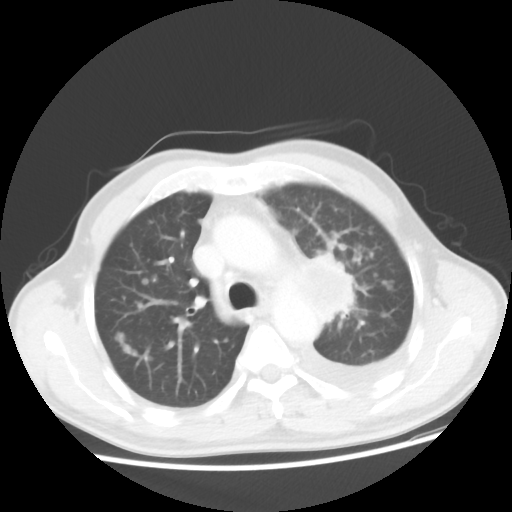
Chest CT, one axial slice; reconstruction kernel STANDARD; lung window (W 1500 / L -600 HU); 512 × 512 image matrix, field of view 362 × 362 mm. Male patient, age 55 years. From the clinical record (not read from this slice): clinical TNM (as recorded): T2 N3 M1a; histopathological grade: G3.
Outlined on this slice (rectangle marked by the reading radiologist):
- lung tumour (recorded histology: squamous cell carcinoma): bounding box [x1, y1, x2, y2] px = [290, 253, 348, 323]